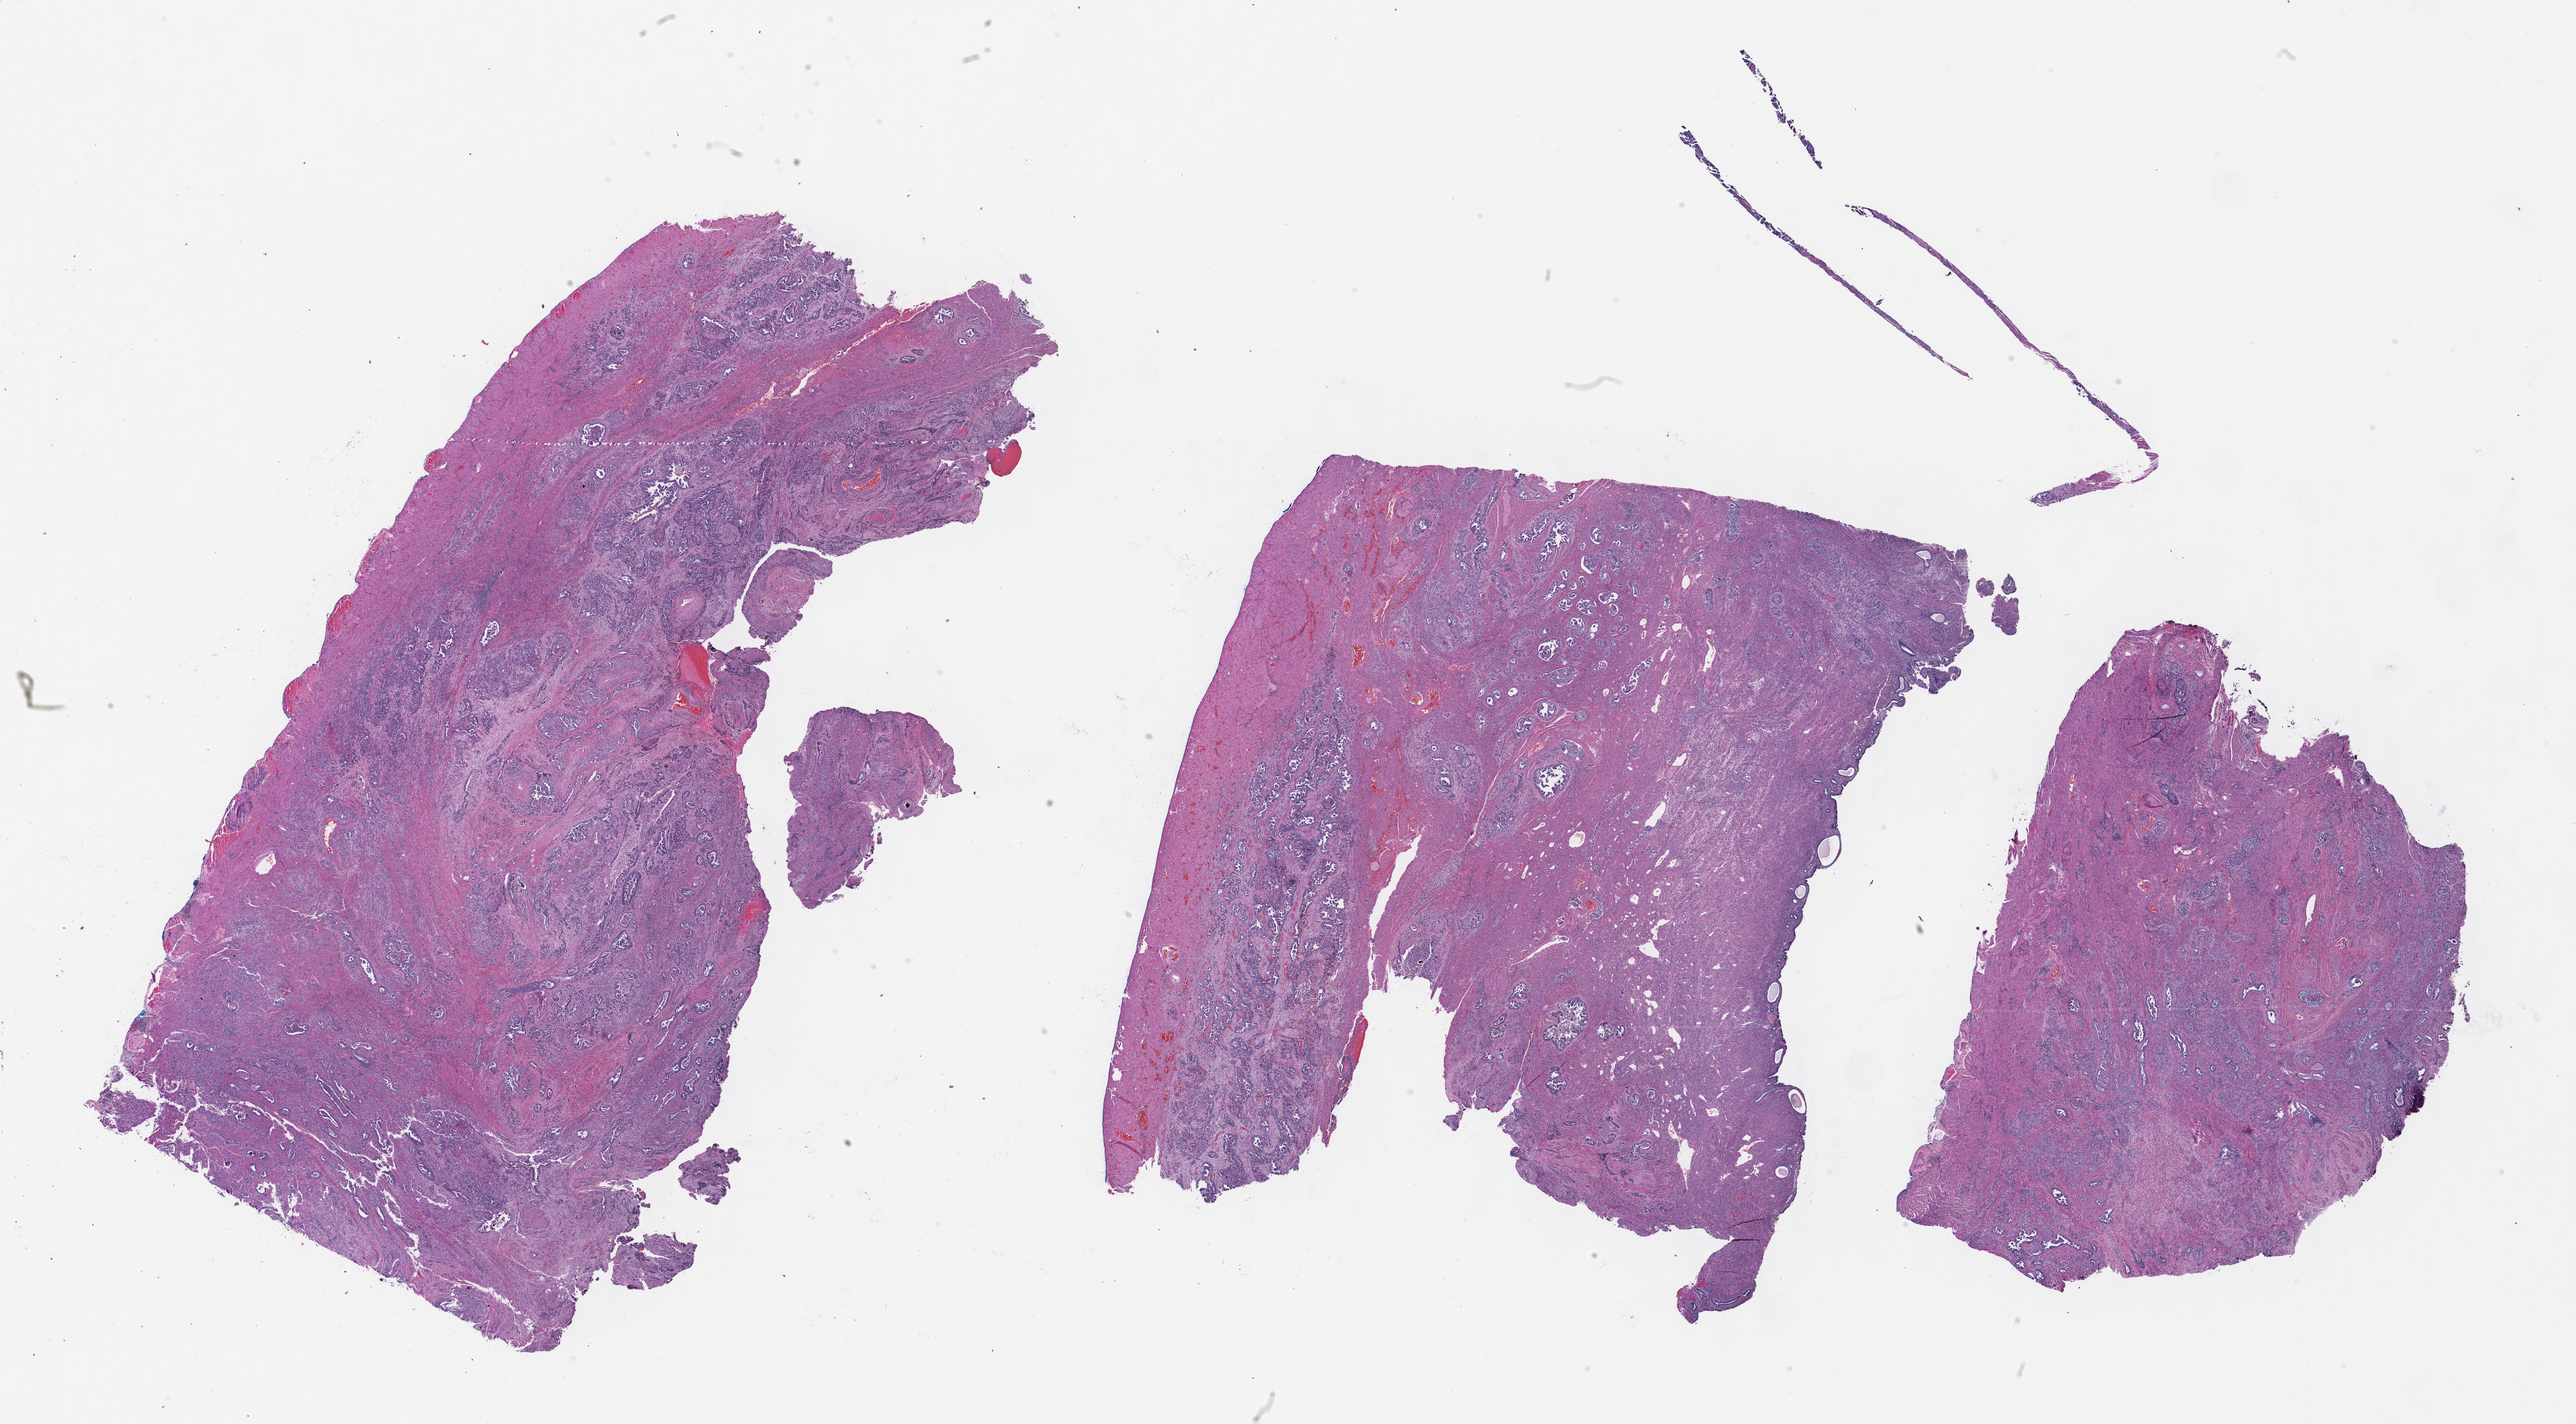
H&E-stained whole-slide image, shown as a low-resolution overview of the whole scanned area (about 32.7 x 18.1 mm, from a 40x scan); formalin-fixed paraffin-embedded (FFPE) diagnostic section; primary tumour sample from the uterus. Female patient; age at initial diagnosis 85 years. Histologic grade: G3 (poorly differentiated).
Histologic diagnosis: Serous cystadenocarcinoma, NOS (fundus uteri). FIGO stage: IIIA.